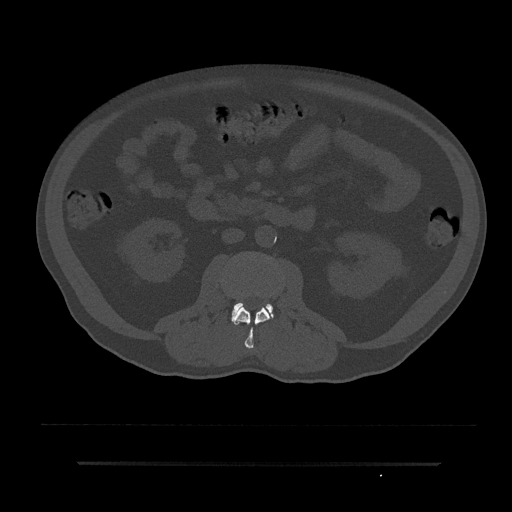
CT including the spine, one axial slice. Position 42 of 797 along the scan axis. Reconstruction kernel Br40s/3. Bone window (W 1800 / L 400 HU). 0.5 mm slice thickness. 512 × 512 image matrix, field of view 464 × 464 mm. Male patient, age 59 years. From the clinical record (not read from this slice): primary cancer: bile ducts; vertebrae with lytic lesions (as recorded): T10.
Outlined on this slice (semi-automatically segmented with operator editing):
- L2 vertebra: bounding box [x1, y1, x2, y2] px = [233, 305, 270, 349]
- L3 vertebra: [232, 302, 273, 321]